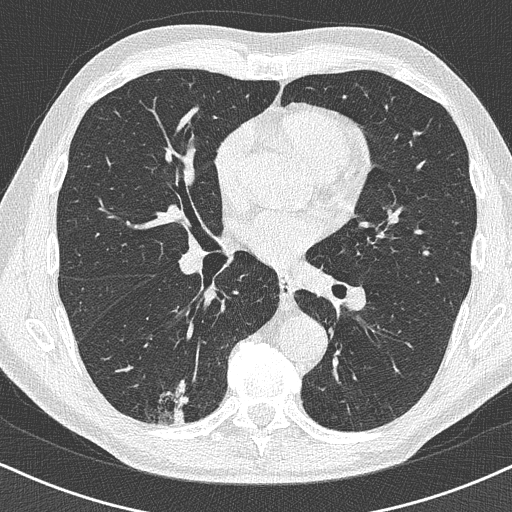
Axial slice from a low-dose chest CT screening exam. Baseline screening round. Lung window (W 1500 / L -600 HU). Slice 215 of 438 in the series. Male participant, aged 63 years at enrolment. Former smoker at enrolment.
Expert-annotated lung lesion, bounding box [x1, y1, x2, y2] px = [134, 367, 206, 429]. Reader record for this screening exam (exam-level; its link to the box is not recorded): non-calcified nodule or mass ≥4 mm, right lower lobe, 16 × 13 mm, poorly defined margins. Later outcome: lung cancer diagnosed 74 days after this screen — adenocarcinoma, NOS, right lower lobe, moderately differentiated (G2), stage IA (AJCC 6th edition), 20 mm at pathology.